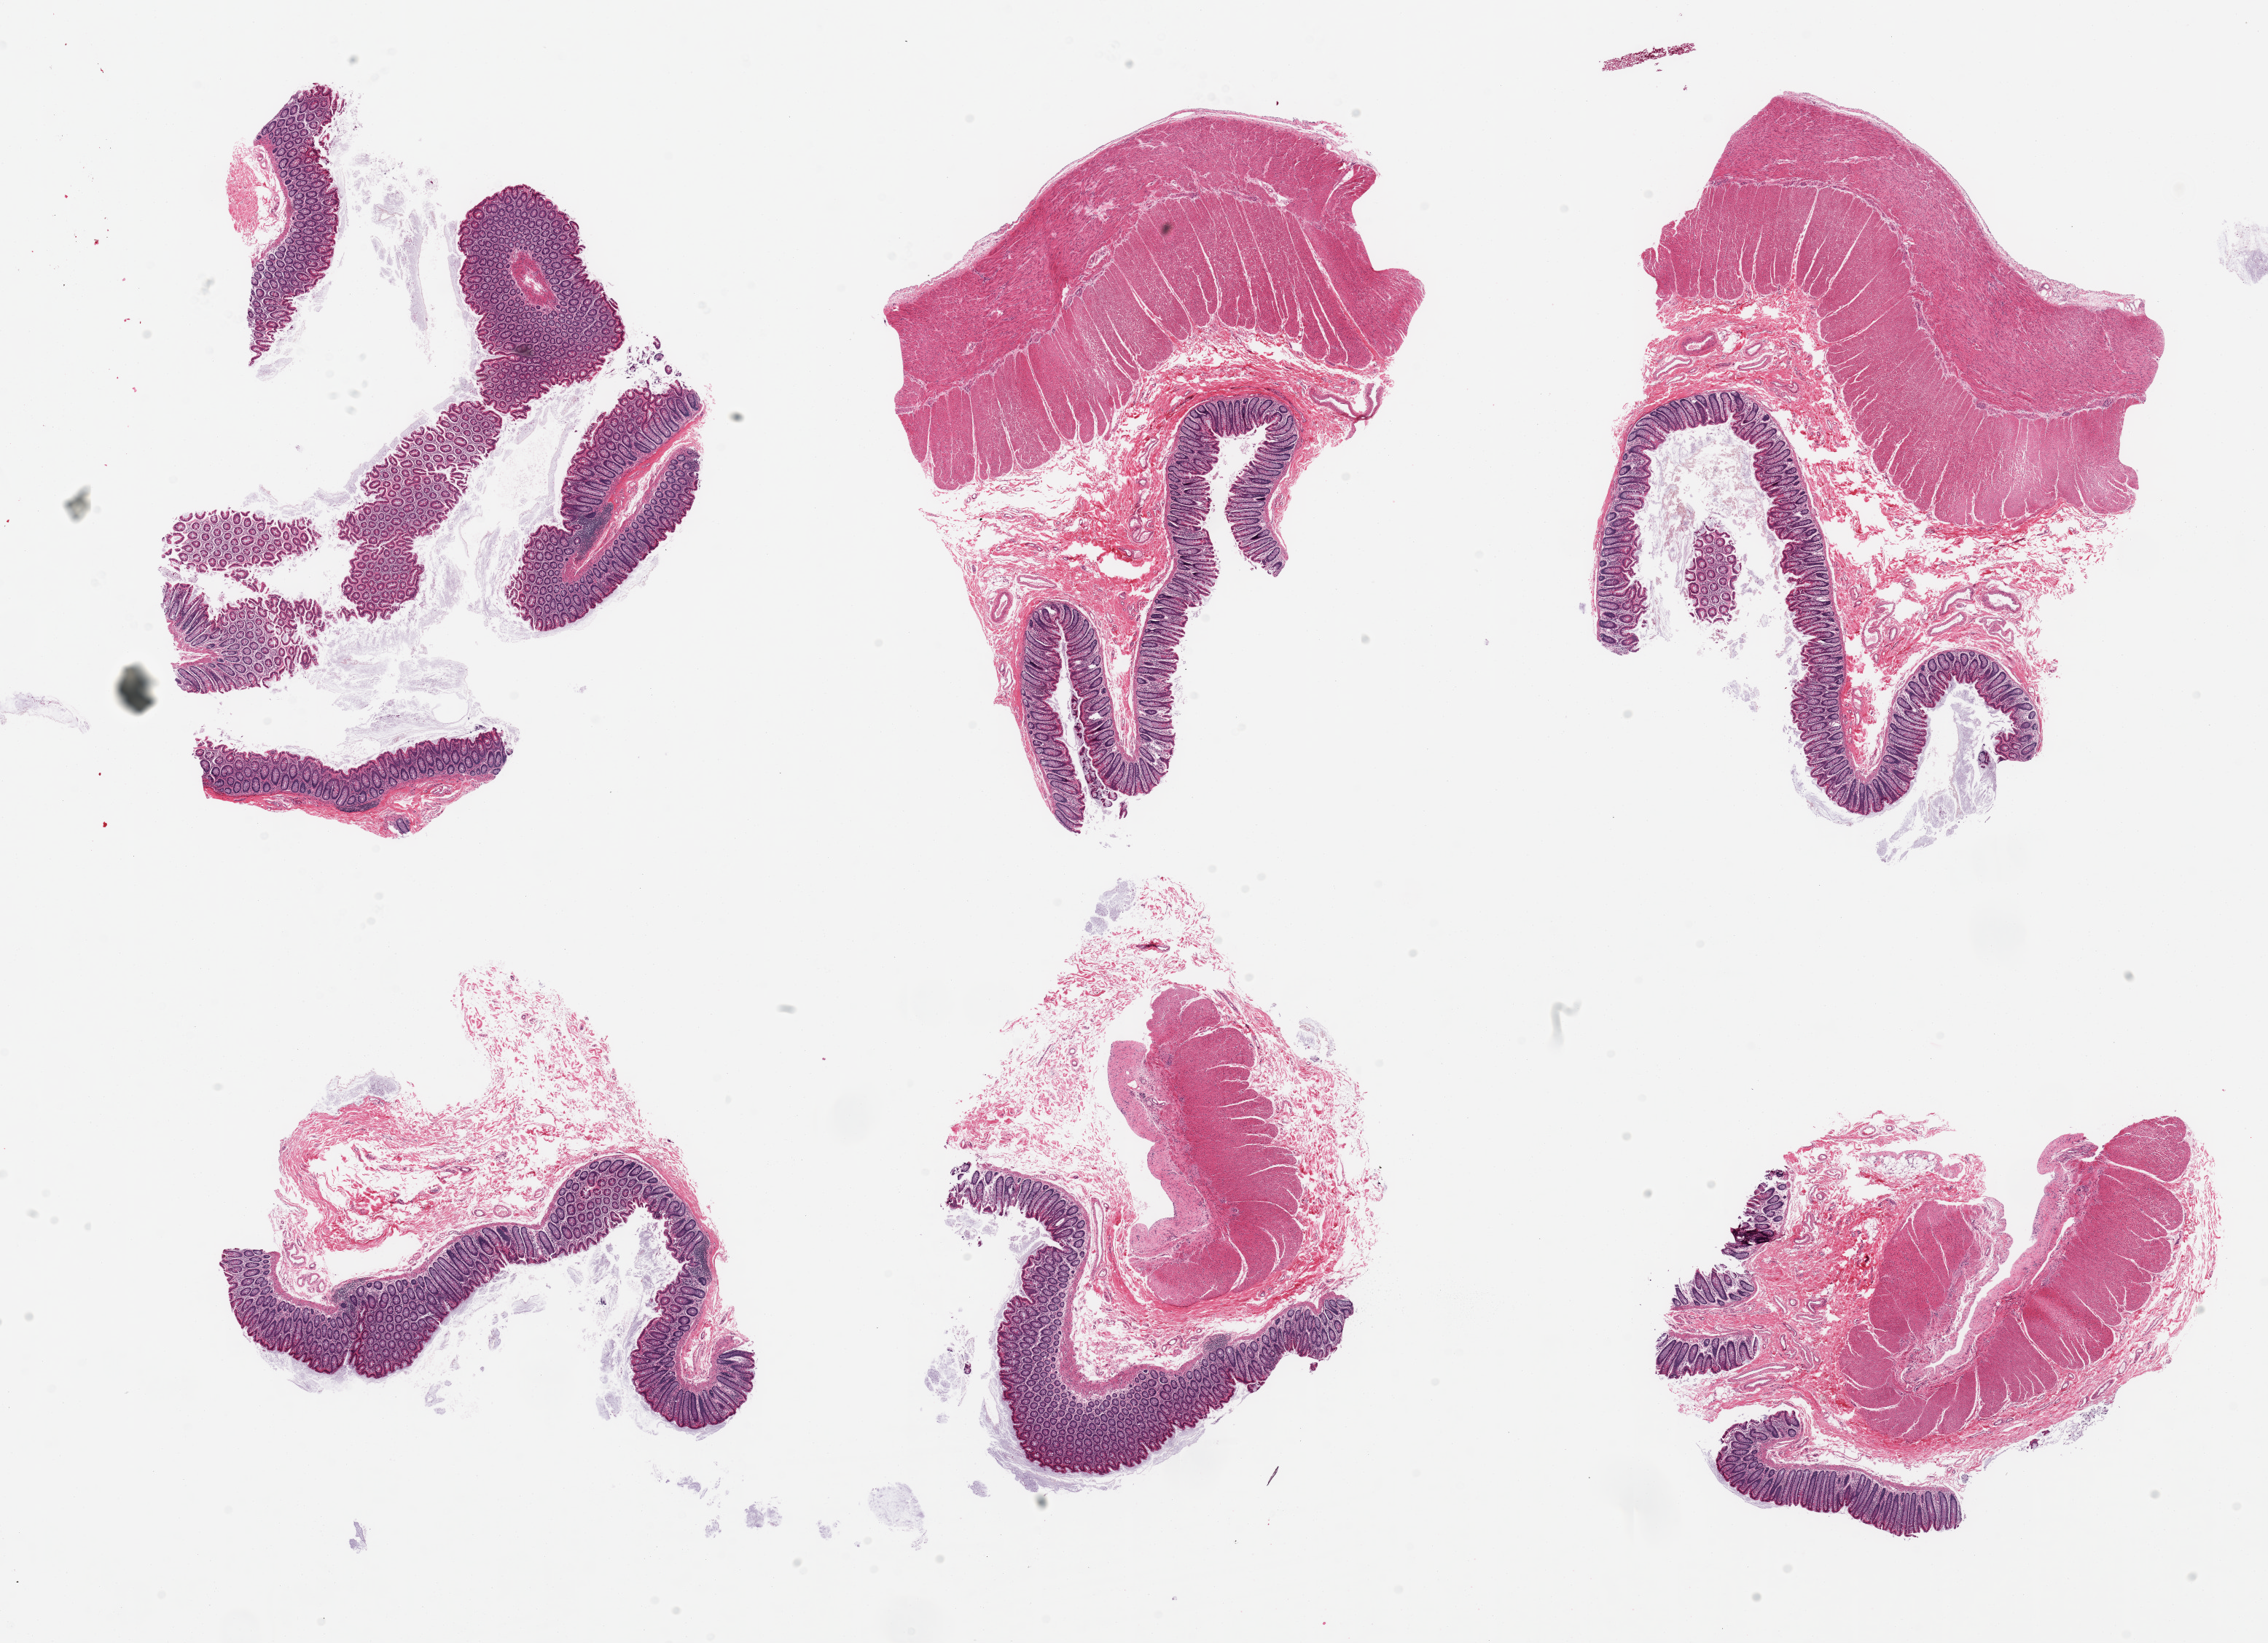
Digitized haematoxylin and eosin-stained section — a low-resolution overview of the entire scanned area, about 24.6 x 17.8 mm (acquisition: 20x scan), PAXgene-fixed, paraffin-embedded tissue, section of transverse colon (target tissue), tissue donor sample.
• reviewer comment on this tissue sample: 6 pieces, target mucosa well- fixed, up to ~0.5mm, ~10-80% thickness